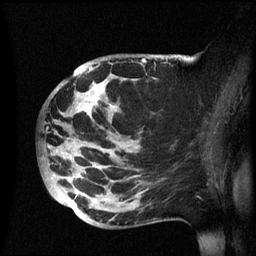
Breast MRI (dynamic contrast-enhanced), one sagittal slice; position 34 of 60 along the scan axis; dynamic contrast-enhanced series, image 2 of 3 at this slice position (ordered by acquisition); 1.5 T; TE 4.2 ms, TR 8.4 ms; 2.4 mm slice thickness; 256 × 256 image matrix, field of view 230 × 230 mm. Female patient, age 49 years.
Outlined on this slice (semi-automatic segmentation, software-assisted and operator-edited):
- analysis volume of interest (the breast-tissue region the enhancement analysis was run in; not a lesion): box from (x=41, y=54) to (x=174, y=228) px
- tumour enhancement mask (voxels above the 70 % enhancement threshold inside the analysis volume of interest): (x=78, y=89)–(x=138, y=150)